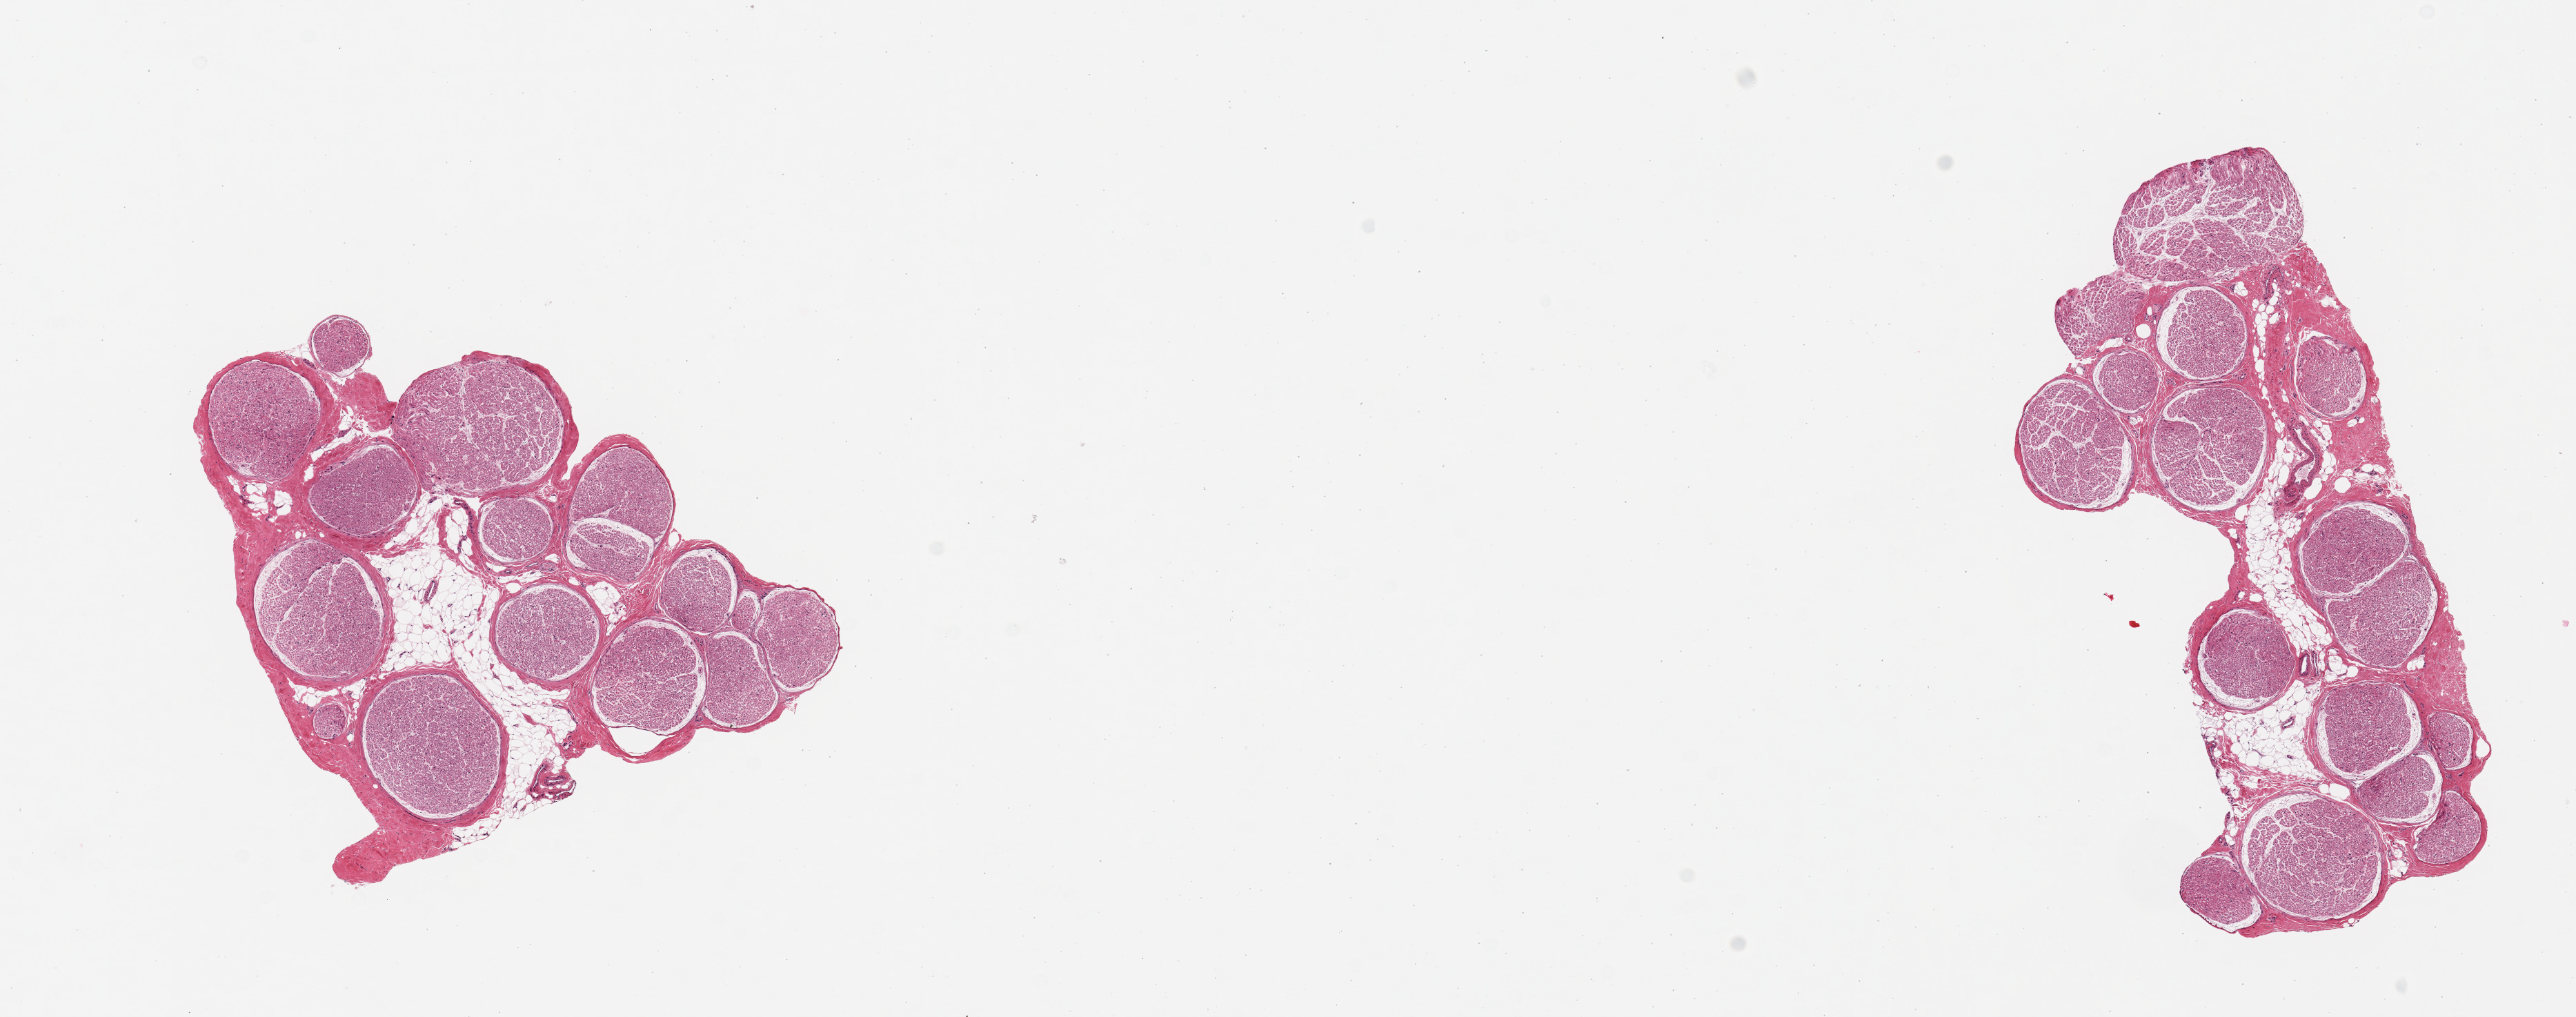
Whole-slide image, hematoxylin and eosin (H&E) stain, a low-resolution overview of the entire scanned area, about 14.8 x 5.8 mm; PAXgene-fixed paraffin-embedded (PFPE) section; sampled site (target tissue): tibial nerve; donor tissue sample.
Reviewer comment on this tissue sample: 2 pieces; both include ~15% internal fat.